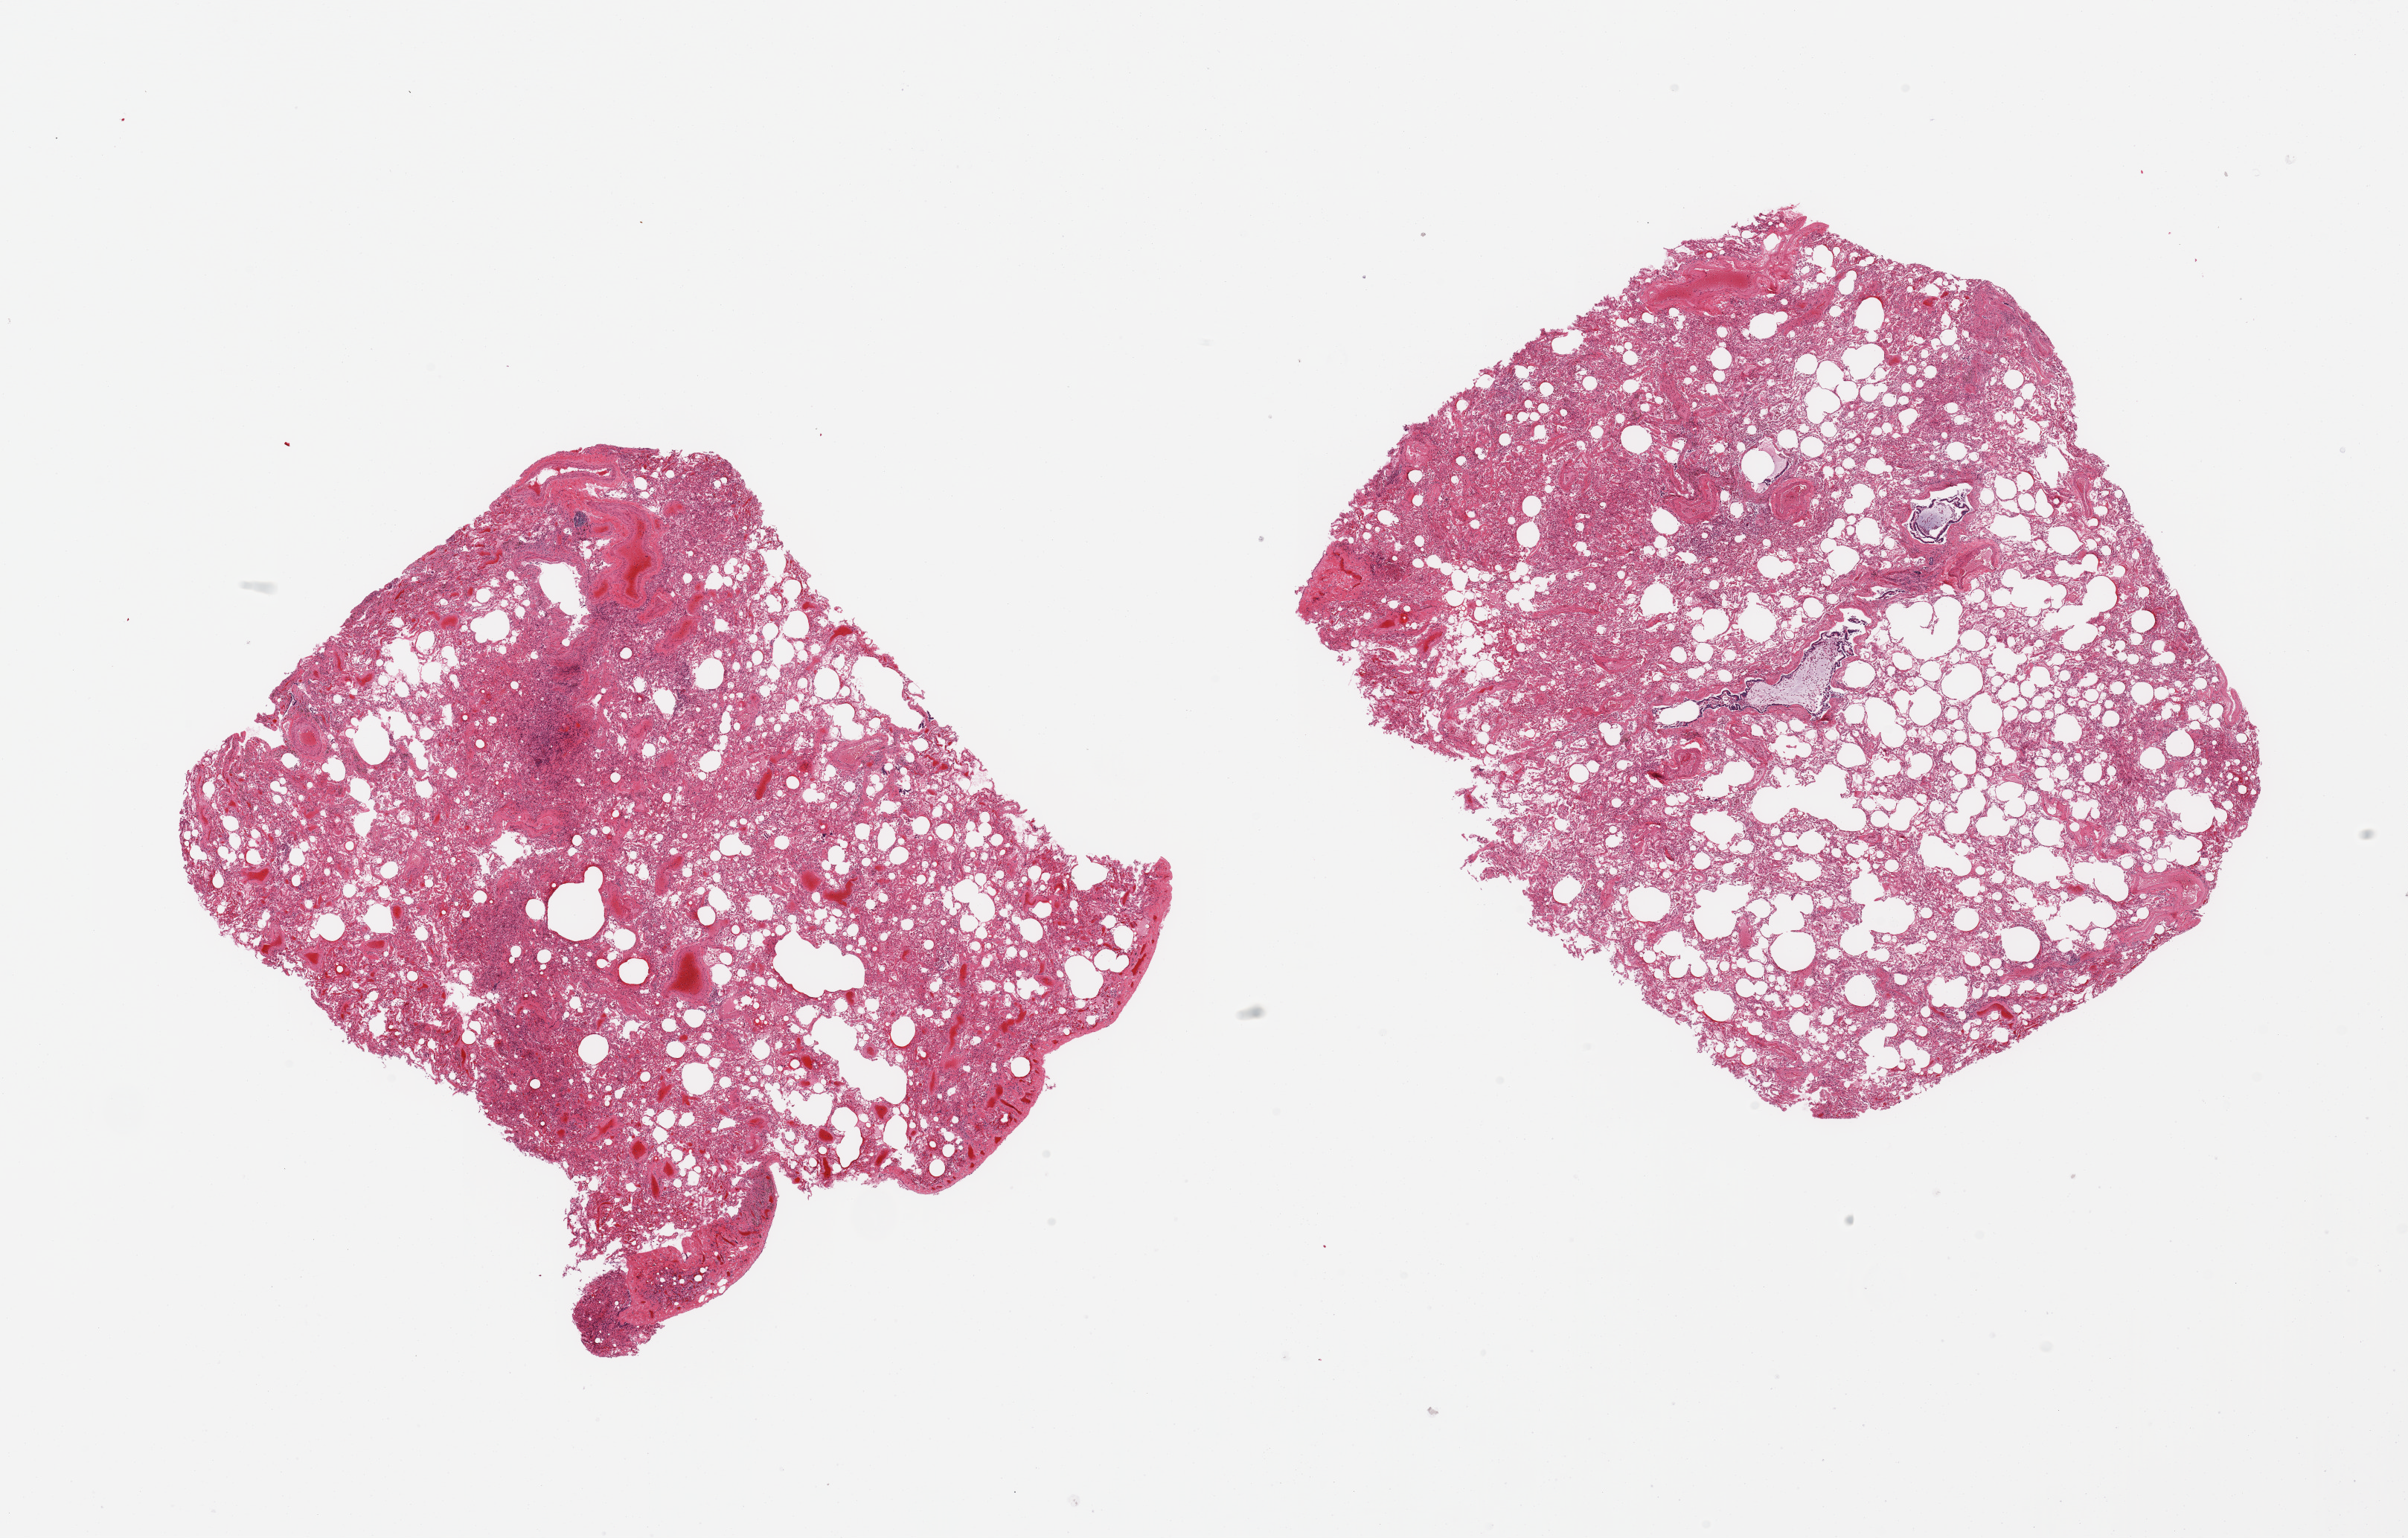
Whole-slide image, hematoxylin and eosin (H&E) stain — a low-resolution overview of the entire scanned area, about 25.6 x 16.3 mm; PAXgene-fixed paraffin-embedded (PFPE) section; sampled site (target tissue): lung; donor tissue sample. Donor: male.
Review note (as recorded): 2 pieces; patchy emphysema; moderate number of alveolar macrophages.